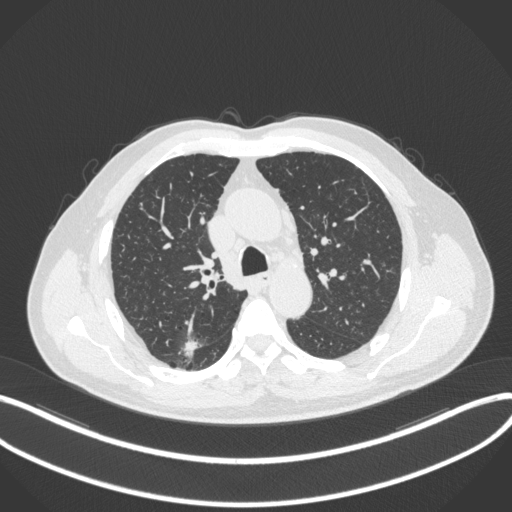
Chest CT, one axial slice. Slice 255 of 366 in the series (ordered by position). Reconstruction kernel B31f. 120 kVp. Lung window (W 1500 / L -600 HU). 1 mm slice thickness. 512 × 512 image matrix, field of view 400 × 400 mm. Male patient, age 69 years. From the clinical record (not read from this slice): clinical TNM (as recorded): T1b N0 M0; histopathological grade: G2-3.
Structures marked on this image (bounding box drawn by a radiologist):
- lung tumour (recorded histology: adenocarcinoma): box from (x=180, y=336) to (x=202, y=364) px